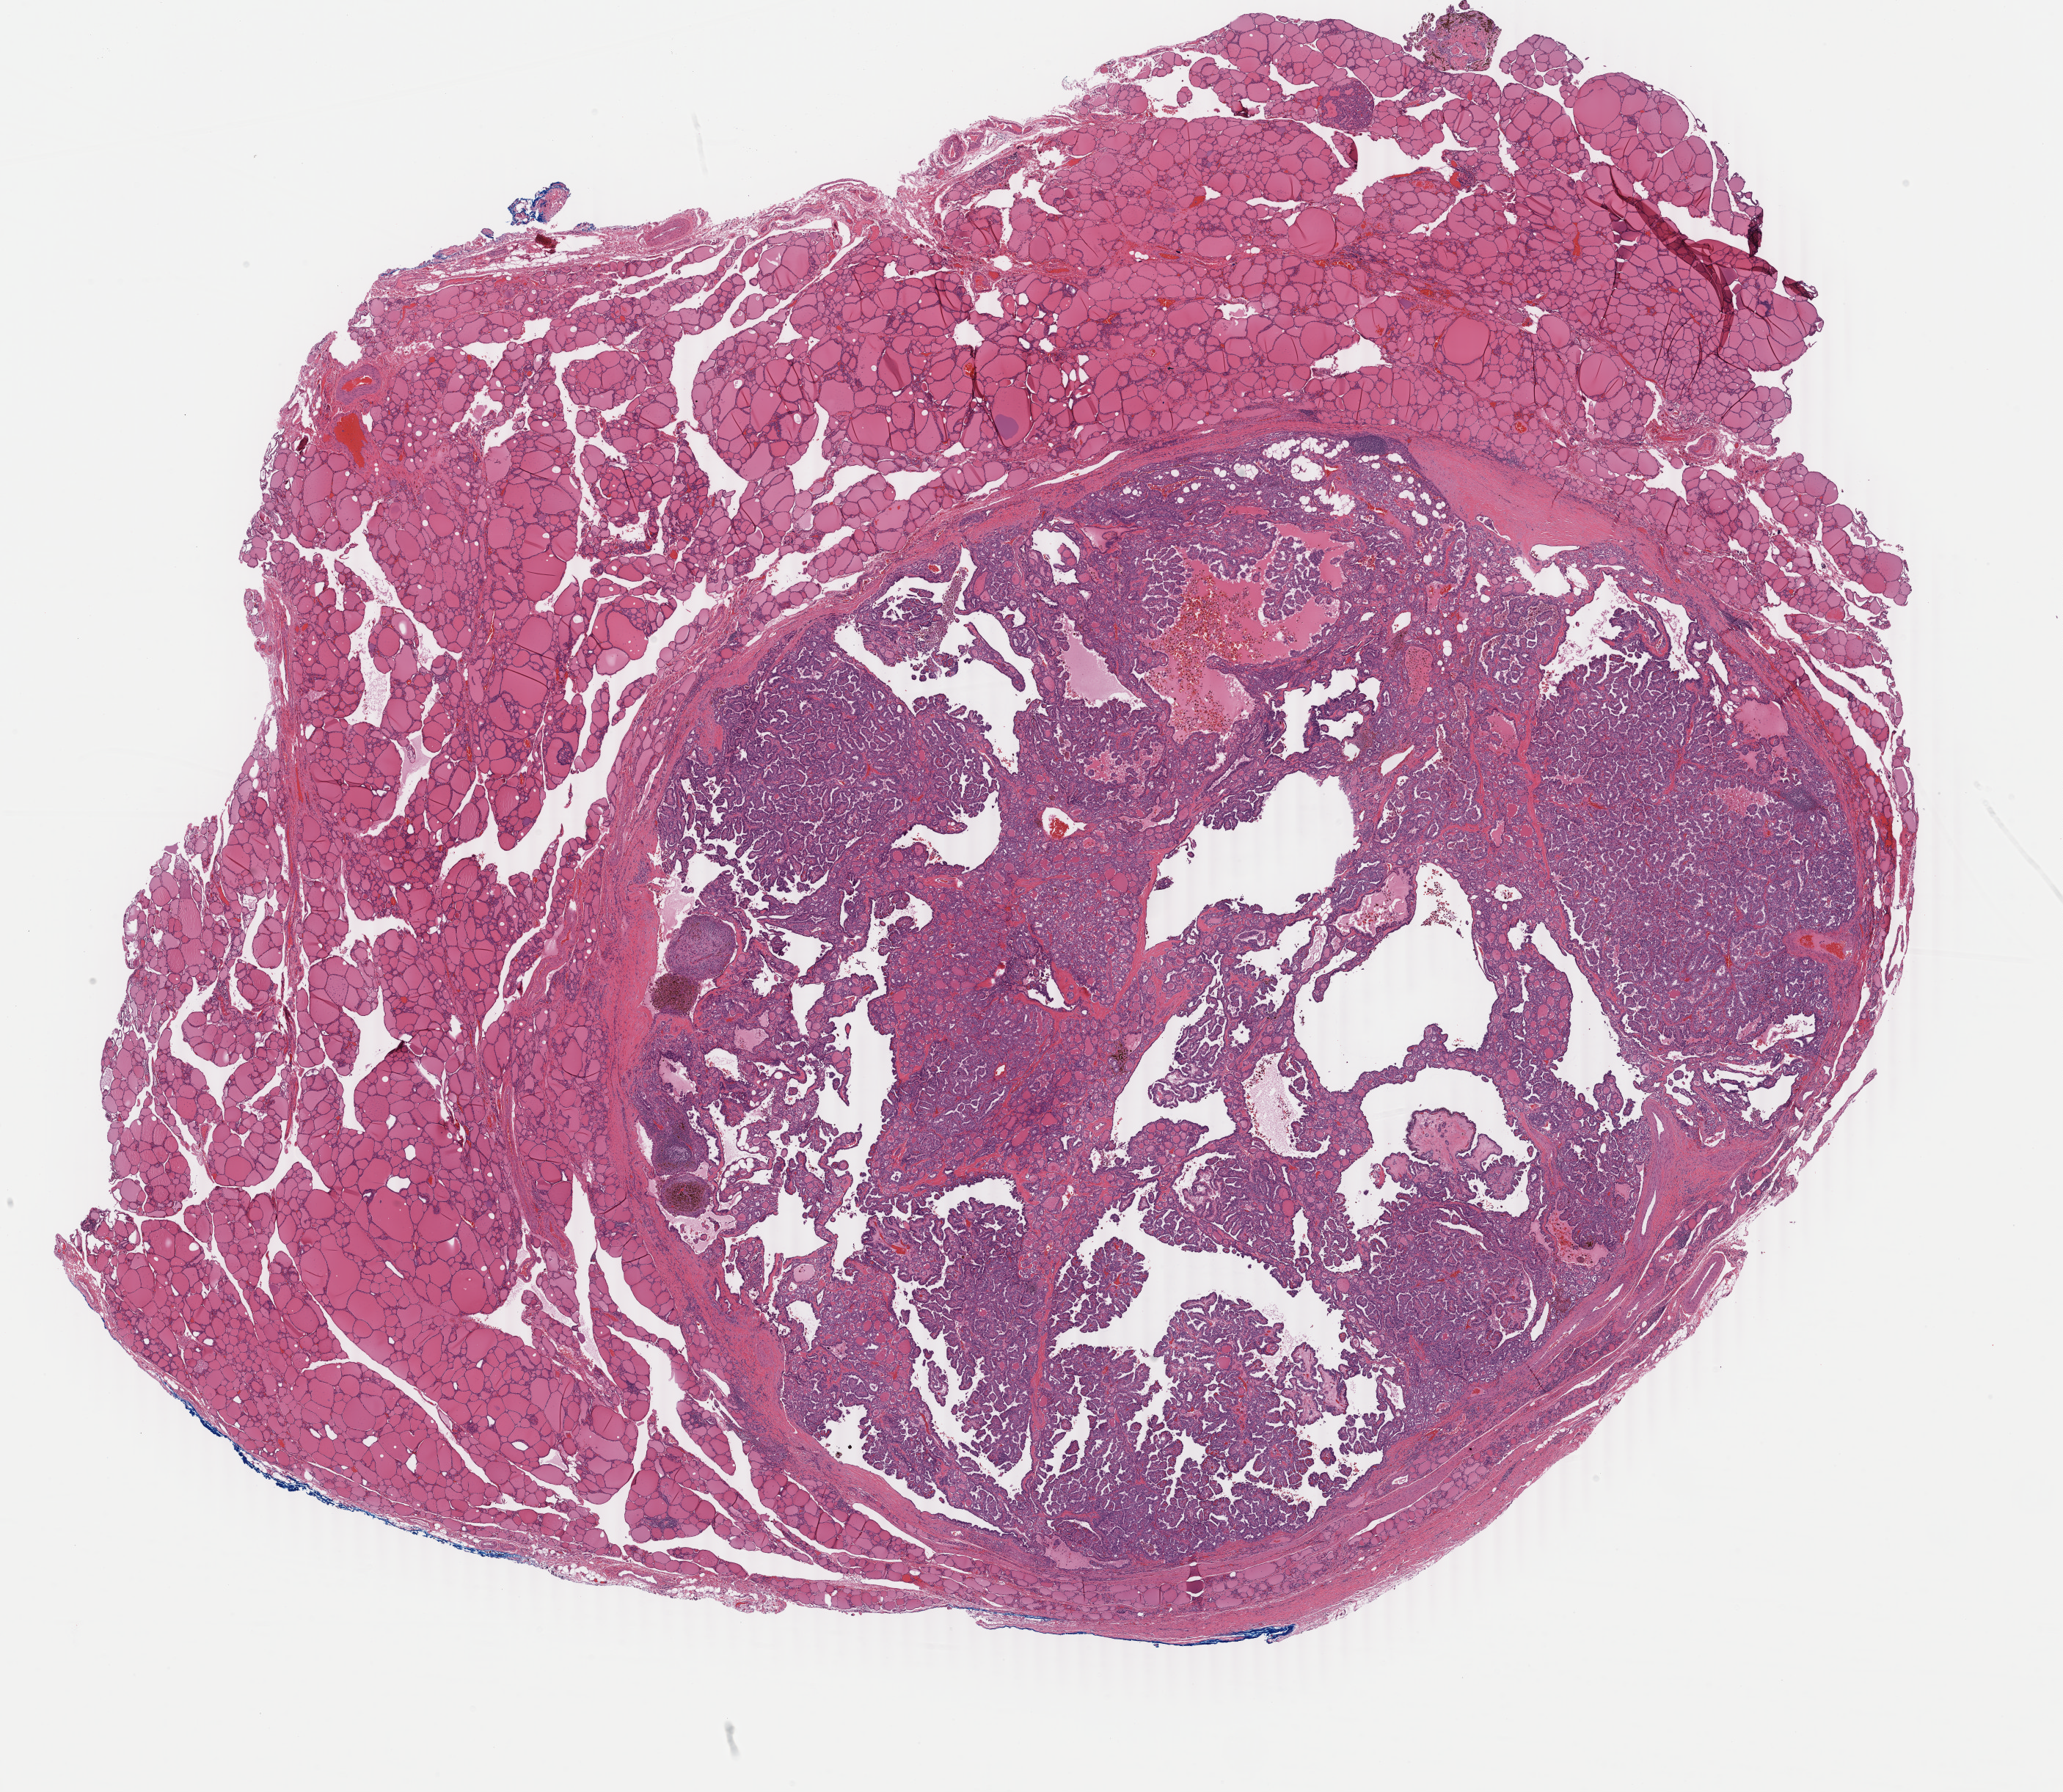
Whole-slide histology image, Hematoxylin and eosin (H&E) stained, shown as a low-resolution overview of the whole scanned area (about 22.4 x 19.4 mm); formalin-fixed paraffin-embedded (FFPE) diagnostic section; thyroid, primary tumour sample. Female patient; age at initial diagnosis 61 years.
Pathologic diagnosis: Papillary adenocarcinoma, NOS (thyroid gland).